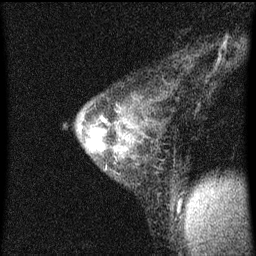
Breast MRI (dynamic contrast-enhanced), one sagittal slice. Position 42 of 60 along the scan axis. Dynamic contrast-enhanced series, image 2 of 4 at this slice position (ordered by acquisition). 1.5 T. TE 4.2 ms, TR 8 ms. 2 mm slice thickness. 256 × 256 image matrix, field of view 180 × 180 mm. Patient: female, 33 years.
Structures marked on this image (semi-automatic segmentation, software-assisted and operator-edited):
- analysis volume of interest (the breast-tissue region the enhancement analysis was run in; not a lesion): bounding box [x1, y1, x2, y2] px = [65, 90, 175, 219]
- tumour enhancement mask (voxels above the 70 % enhancement threshold inside the analysis volume of interest): [100, 116, 106, 123]